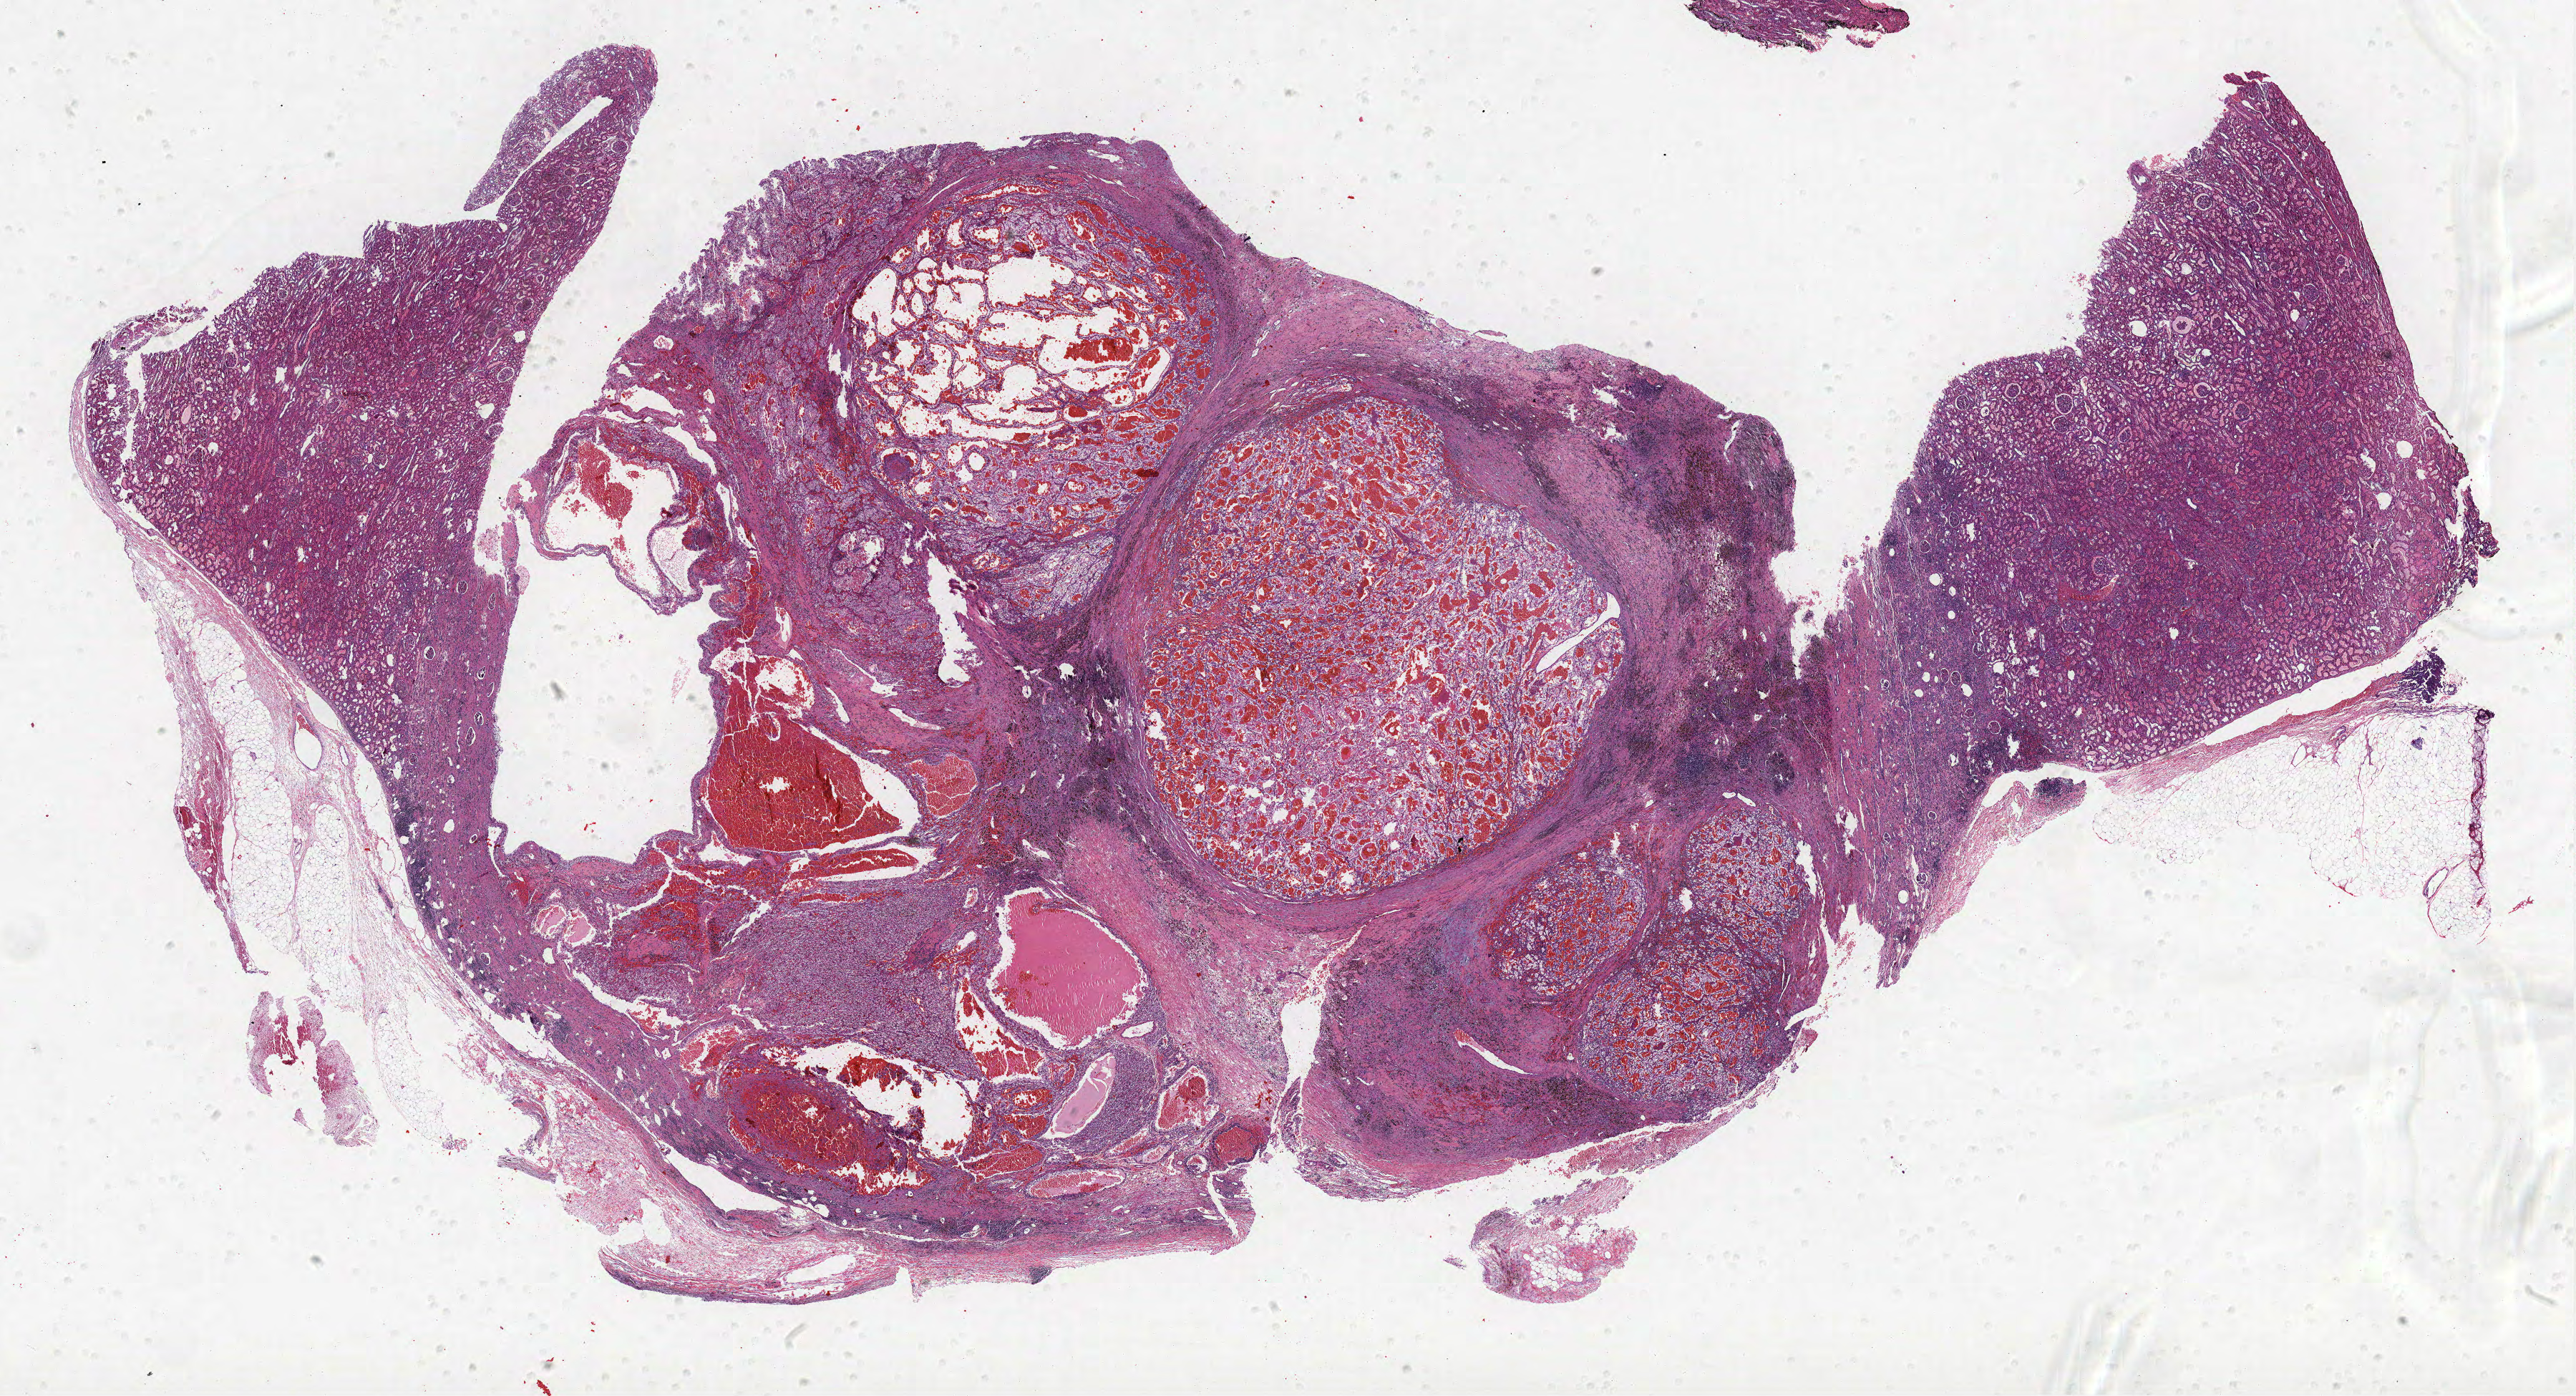
Digitized Hematoxylin and eosin (H&E) stained tissue section (whole slide), low-resolution overview of the scanned area, about 28.8 x 15.6 mm, formalin-fixed paraffin-embedded (FFPE) diagnostic section, primary tumour sample from the kidney. Male, age 46 years at initial diagnosis. Histologic grade: G3 (poorly differentiated).
Laterality: right. Pathologic diagnosis: Clear cell adenocarcinoma, NOS. AJCC pathologic stage: I.